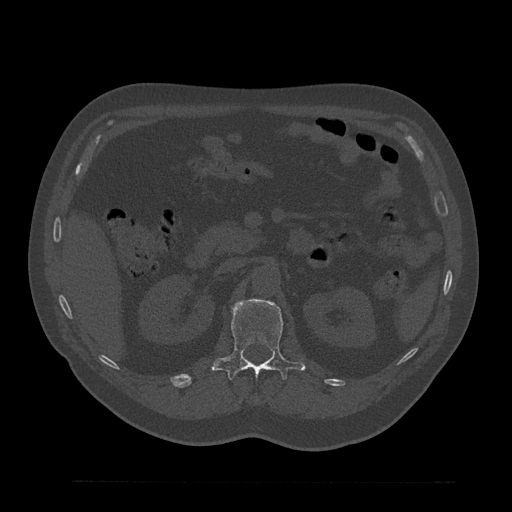
CT including the spine, one axial slice. Slice 169 of 797 in the series (ordered by position). Bone window (W 1800 / L 400 HU). 0.5 mm slice thickness. 512 × 512 image matrix, field of view 430 × 430 mm. Patient: male, 61 years. Case-level facts recorded for this patient, not image findings: primary cancer: prostate.
Outlined on this slice (semi-automatic segmentation, software-assisted and operator-edited):
- L1 vertebra: bounding box (x1, y1, x2, y2) in pixels: (211, 299, 305, 381)